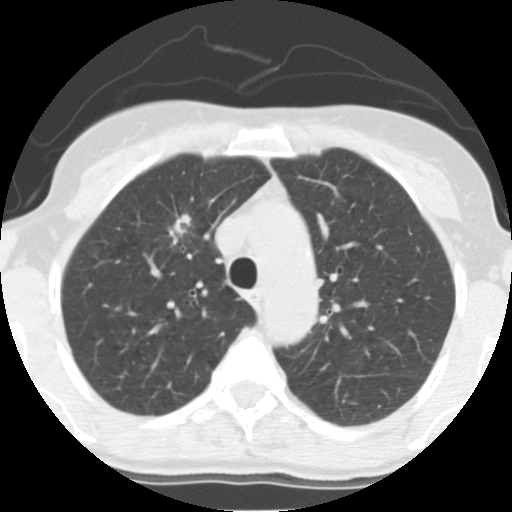
Low-dose screening chest CT, one axial slice; slice 101 of 140 in the series (ordered by position); 140 kVp; lung window (W 1500 / L -600 HU); 2.5 mm slice thickness; 512 × 512 image matrix, field of view 280 × 280 mm.
Outlined on this slice (manually delineated by an expert):
- lesion 1 (tumor, upper lobe of right lung): box from (x=175, y=214) to (x=192, y=237) px